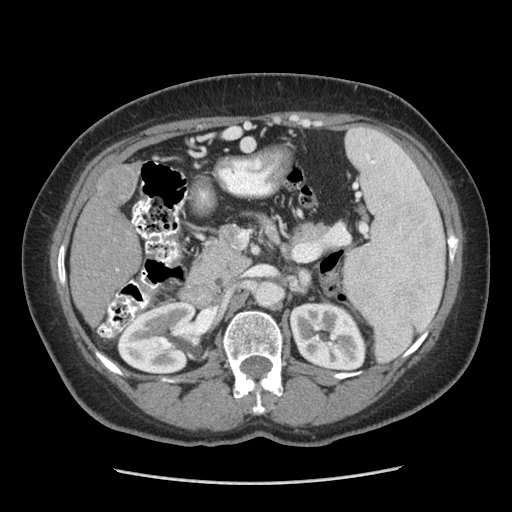
Contrast-enhanced abdominal CT (liver protocol), one axial slice. Position 136 of 185 along the scan axis. Soft-tissue window (W 400 / L 40 HU). 512 × 512 image matrix. From the clinical record (not read from this slice): diagnosis: hepatocellular carcinoma (patient treated with transarterial chemoembolisation; whether this scan precedes or follows treatment is not stated here); TNM stage (as recorded): Stage-I; Child-Pugh class: A; tumour differentiation: poorly differentiated; tumour nodularity: uninodular.
Structures marked on this image (semi-automatically segmented with operator editing):
- liver parenchyma outside the tumour (the mass and vessels are separate outlines, so this box may not span the whole liver): bounding box (x1, y1, x2, y2) in pixels: (70, 164, 140, 304)
- mass: (99, 161, 137, 207)